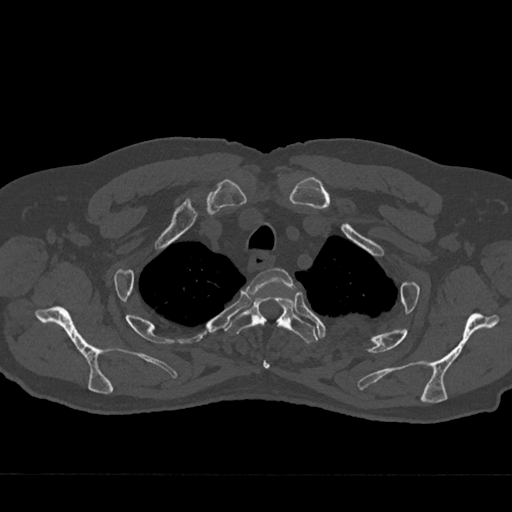
CT including the spine, one axial slice. Position 583 of 797 along the scan axis. Reconstruction kernel Br40s/3. 120 kVp. Bone window (W 1800 / L 400 HU). 0.5 mm slice thickness. 512 × 512 image matrix, field of view 377 × 377 mm. Patient: male, 75 years. Case-level facts recorded for this patient, not image findings: primary cancer: renal.
Outlined on this slice (semi-automatically segmented with operator editing):
- T2 vertebra: bounding box [x1, y1, x2, y2] px = [248, 268, 295, 369]
- T3 vertebra: [227, 296, 318, 343]